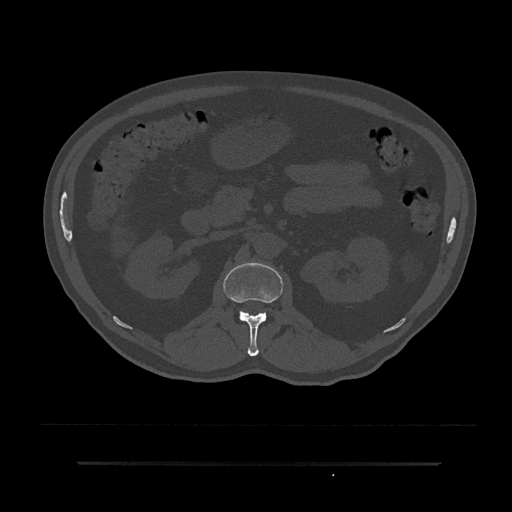
CT including the spine, one axial slice; position 128 of 797 along the scan axis; reconstruction kernel Br40s/3; 120 kVp; bone window (W 1800 / L 400 HU); 0.5 mm slice thickness; 512 × 512 image matrix. Male patient, age 59 years. Case-level facts recorded for this patient, not image findings: primary cancer: bile ducts.
Outlined on this slice (semi-automatically segmented with operator editing):
- L1 vertebra: bounding box (x1, y1, x2, y2) in pixels: (223, 262, 283, 356)